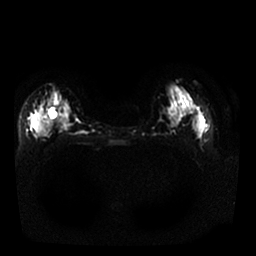
Breast MRI, one axial slice. Slice 12 of 25 in the series (ordered by position). Diffusion-weighted series; image 2 of 4 stored at this slice position (different b-values; order by instance number). 1.5 T. 4 mm slice thickness. 256 × 256 image matrix. Female patient.
Annotated regions visible in this slice (expert manual segmentation):
- tumour on diffusion-weighted imaging: bounding box <30,111,47,137> (left, top, right, bottom; pixels)